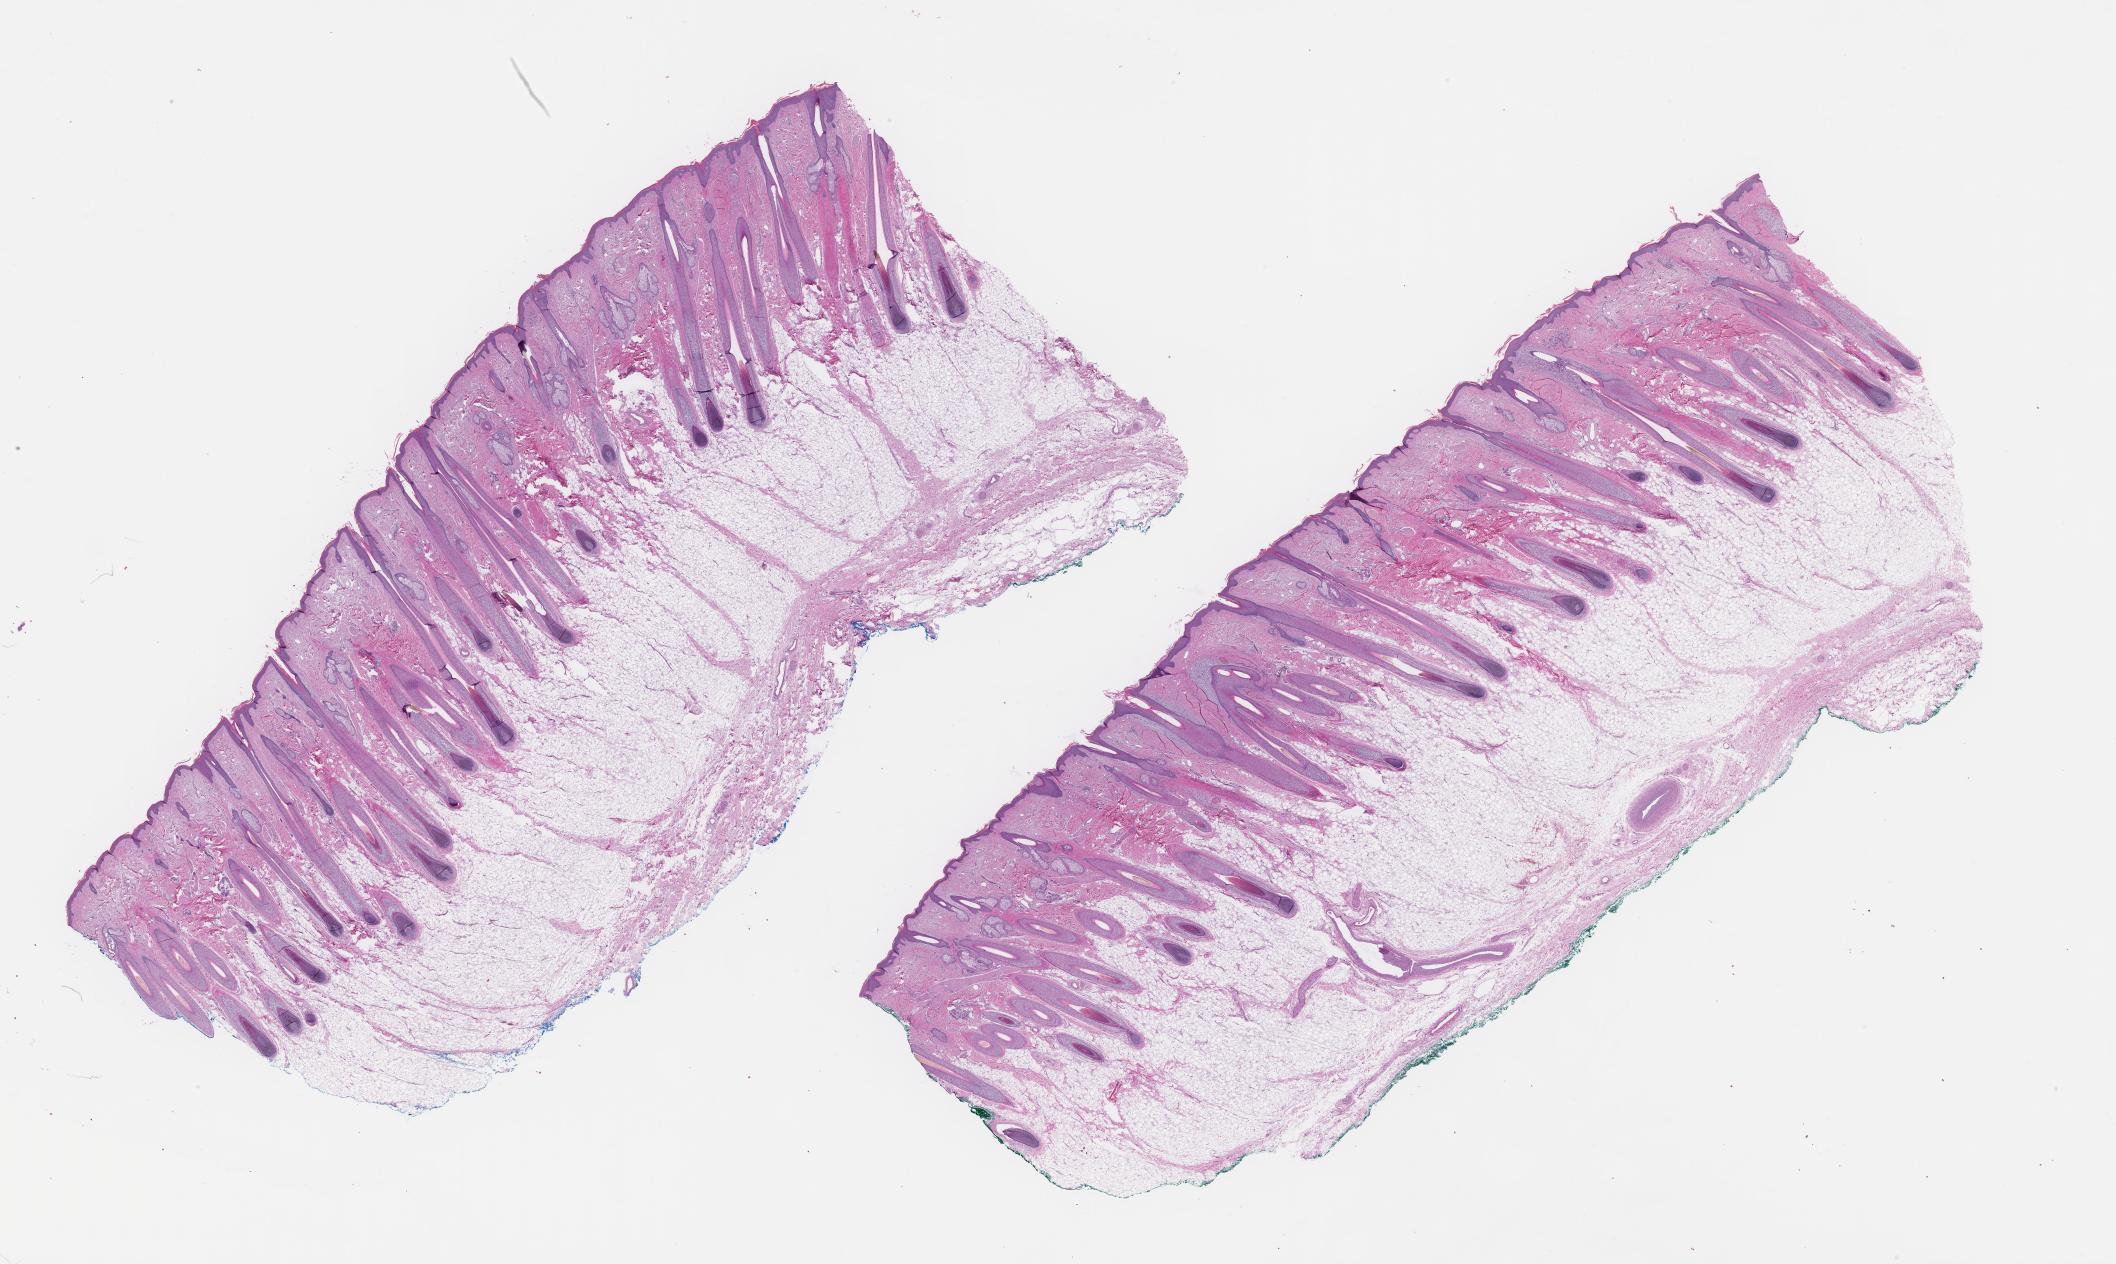
Digitized hematoxylin and eosin (H&E)-stained section, low-resolution overview of the scanned area, about 34.2 x 20.4 mm, FFPE section, tissue site: skin, specimen time point: archival tissue. Patient sex: female.
• this section: primary tumor
• diagnosis: Melanoma